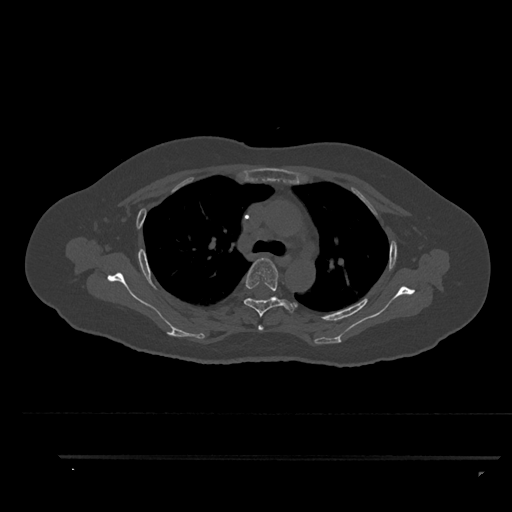
CT including the spine, one axial slice; slice 642 of 797 in the series (ordered by position); reconstruction kernel Br40s/3; 120 kVp; bone window (W 1800 / L 400 HU); 0.5 mm slice thickness; 512 × 512 image matrix, field of view 408 × 408 mm. Female patient, age 44 years. From the clinical record (not read from this slice): primary cancer: renal; vertebrae with lytic lesions (as recorded): L1.
Annotated regions visible in this slice (semi-automatic segmentation, software-assisted and operator-edited):
- T3 vertebra: bounding box [x1, y1, x2, y2] px = [258, 325, 264, 331]
- T4 vertebra: [244, 258, 297, 317]